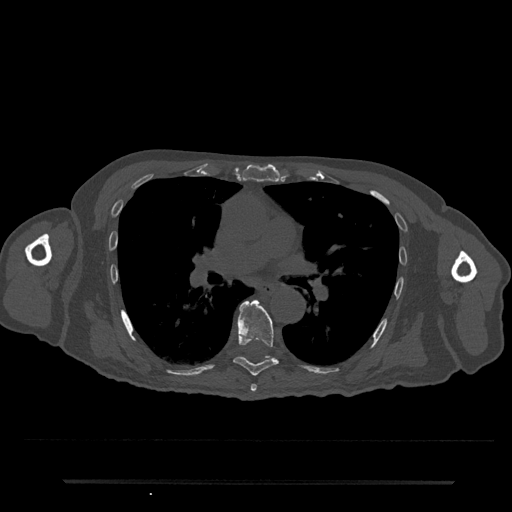
CT including the spine, one axial slice. Position 476 of 797 along the scan axis. Reconstruction kernel Br40s/3. 120 kVp. Bone window (W 1800 / L 400 HU). 512 × 512 image matrix. Patient: male, 74 years. Case-level facts recorded for this patient, not image findings: primary cancer: prostate.
Structures marked on this image (semi-automatically segmented with operator editing):
- T6 vertebra: box from (x=250, y=384) to (x=257, y=392) px
- T7 vertebra: (x=233, y=300)–(x=279, y=376)
- T8 vertebra: (x=265, y=356)–(x=273, y=360)